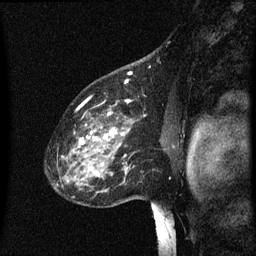
Breast MRI (dynamic contrast-enhanced), one sagittal slice; position 44 of 60 along the scan axis; dynamic contrast-enhanced series, image 2 of 3 at this slice position (ordered by acquisition); 1.5 T; TE 4.2 ms, TR 8 ms; 2 mm slice thickness; 256 × 256 image matrix, field of view 200 × 200 mm. Female patient, age 60 years.
Structures marked on this image (semi-automatically segmented with operator editing):
- analysis volume of interest (the breast-tissue region the enhancement analysis was run in; not a lesion): bounding box [x1, y1, x2, y2] px = [53, 100, 142, 197]
- tumour enhancement mask (voxels above the 70 % enhancement threshold inside the analysis volume of interest): [75, 100, 131, 177]